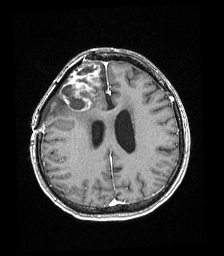
Brain MRI from a brain-tumour surgery series, one axial slice; position 73 of 192 along the scan axis; T1-weighted post-contrast; 224 × 256 image matrix. From the clinical record (not read from this slice): histopathology: Astrocytoma; WHO grade: 4; IDH mutation: yes; tumour location: Right superficial frontal.
Annotated regions visible in this slice (manually delineated by an expert):
- tumour: bounding box [x1, y1, x2, y2] px = [60, 62, 101, 112]